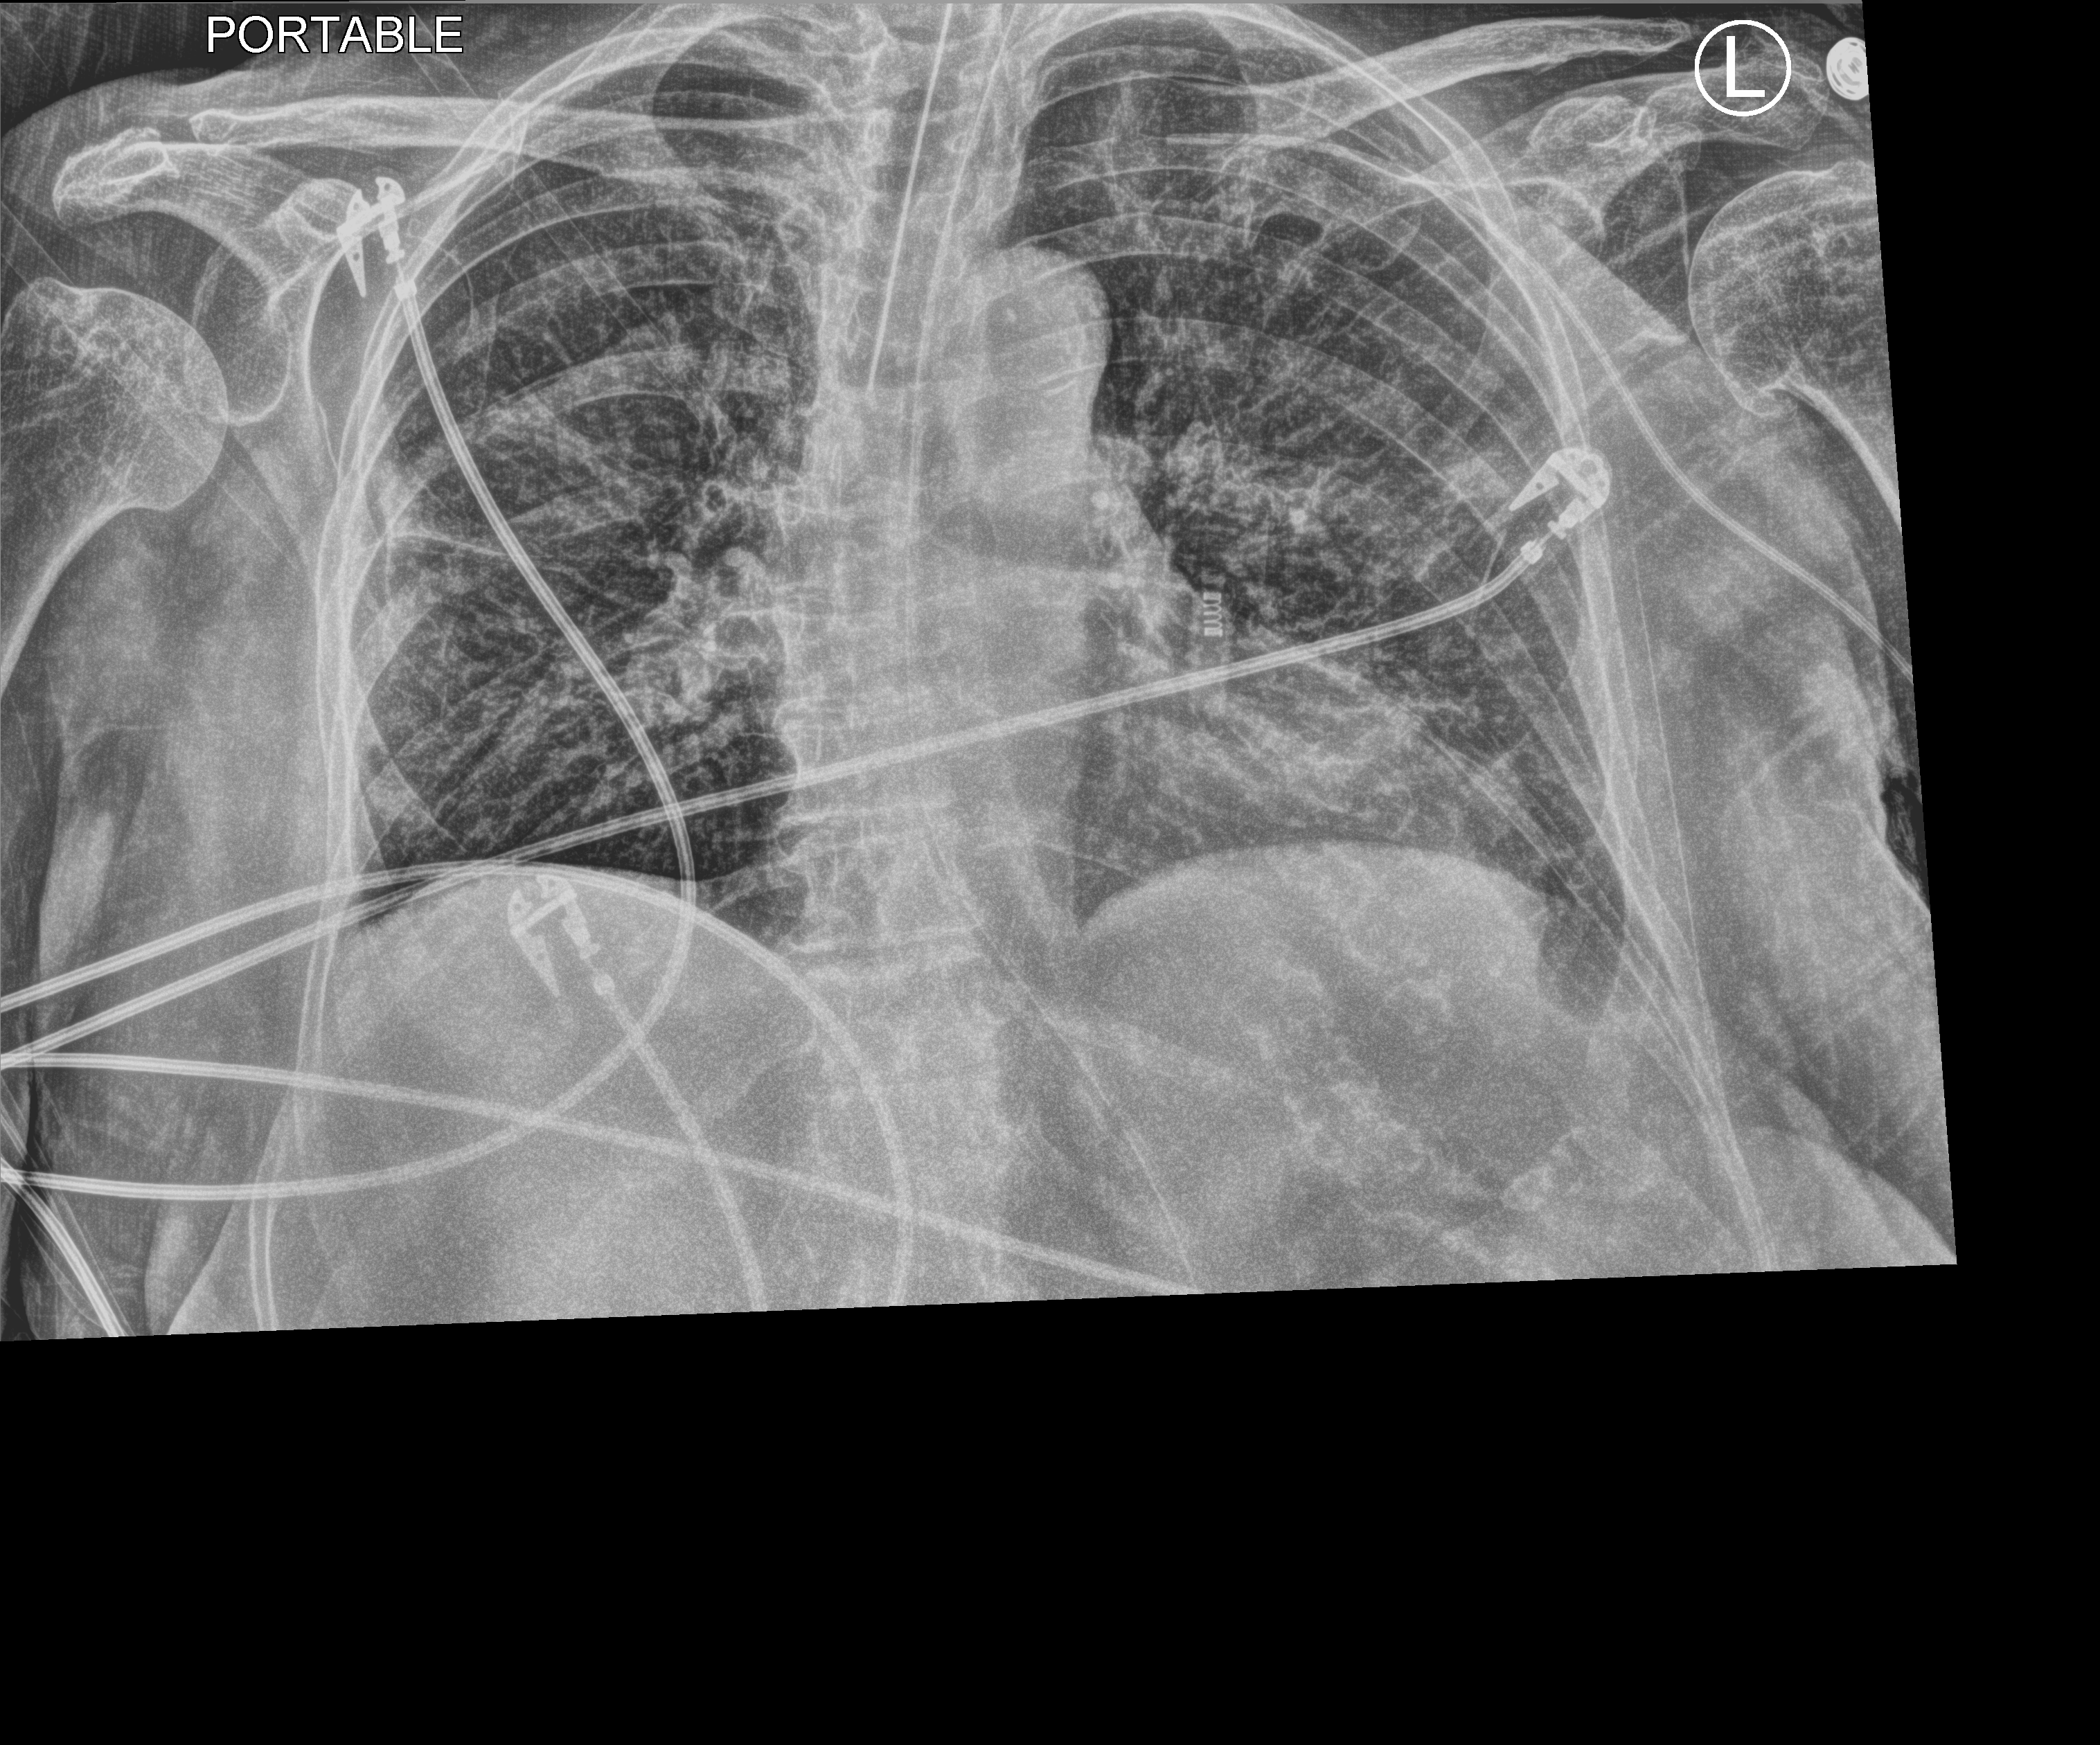
Chest X-ray (portable), anteroposterior (AP) projection. Female patient hospitalised with COVID-19, age 75–90 years.
Admission-level facts for this patient (not findings on this image; timing relative to this image not recorded):
- length of hospital stay: 82 days
- admitted to intensive care during this hospital stay: yes
- mechanically ventilated during this hospital stay: yes